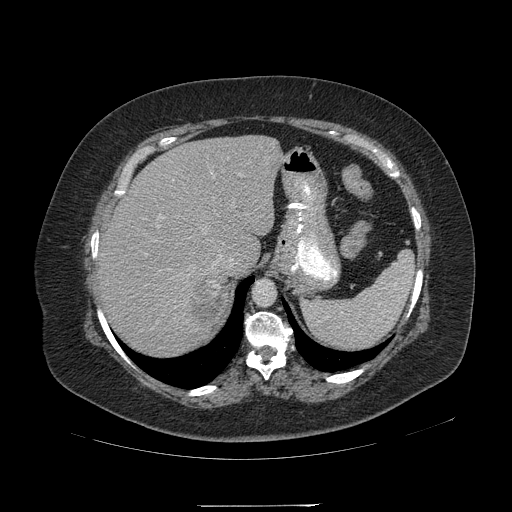
Contrast-enhanced abdominal CT, one axial slice. 120 kVp. Intravenous contrast given. Soft-tissue window (W 400 / L 40 HU). 1.25 mm slice thickness. 512 × 512 image matrix, field of view 453 × 453 mm. Female patient, age 55 years. Case-level facts recorded for this patient, not image findings: diagnosis: adrenocortical carcinoma; tumour side: right adrenal; tumour size at pathology: 11 cm; Ki-67 index: 20 %; stage (as recorded): 2.
Annotated regions visible in this slice (semi-automatic segmentation, software-assisted and operator-edited):
- mass: bounding box <189,282,222,325> (left, top, right, bottom; pixels)